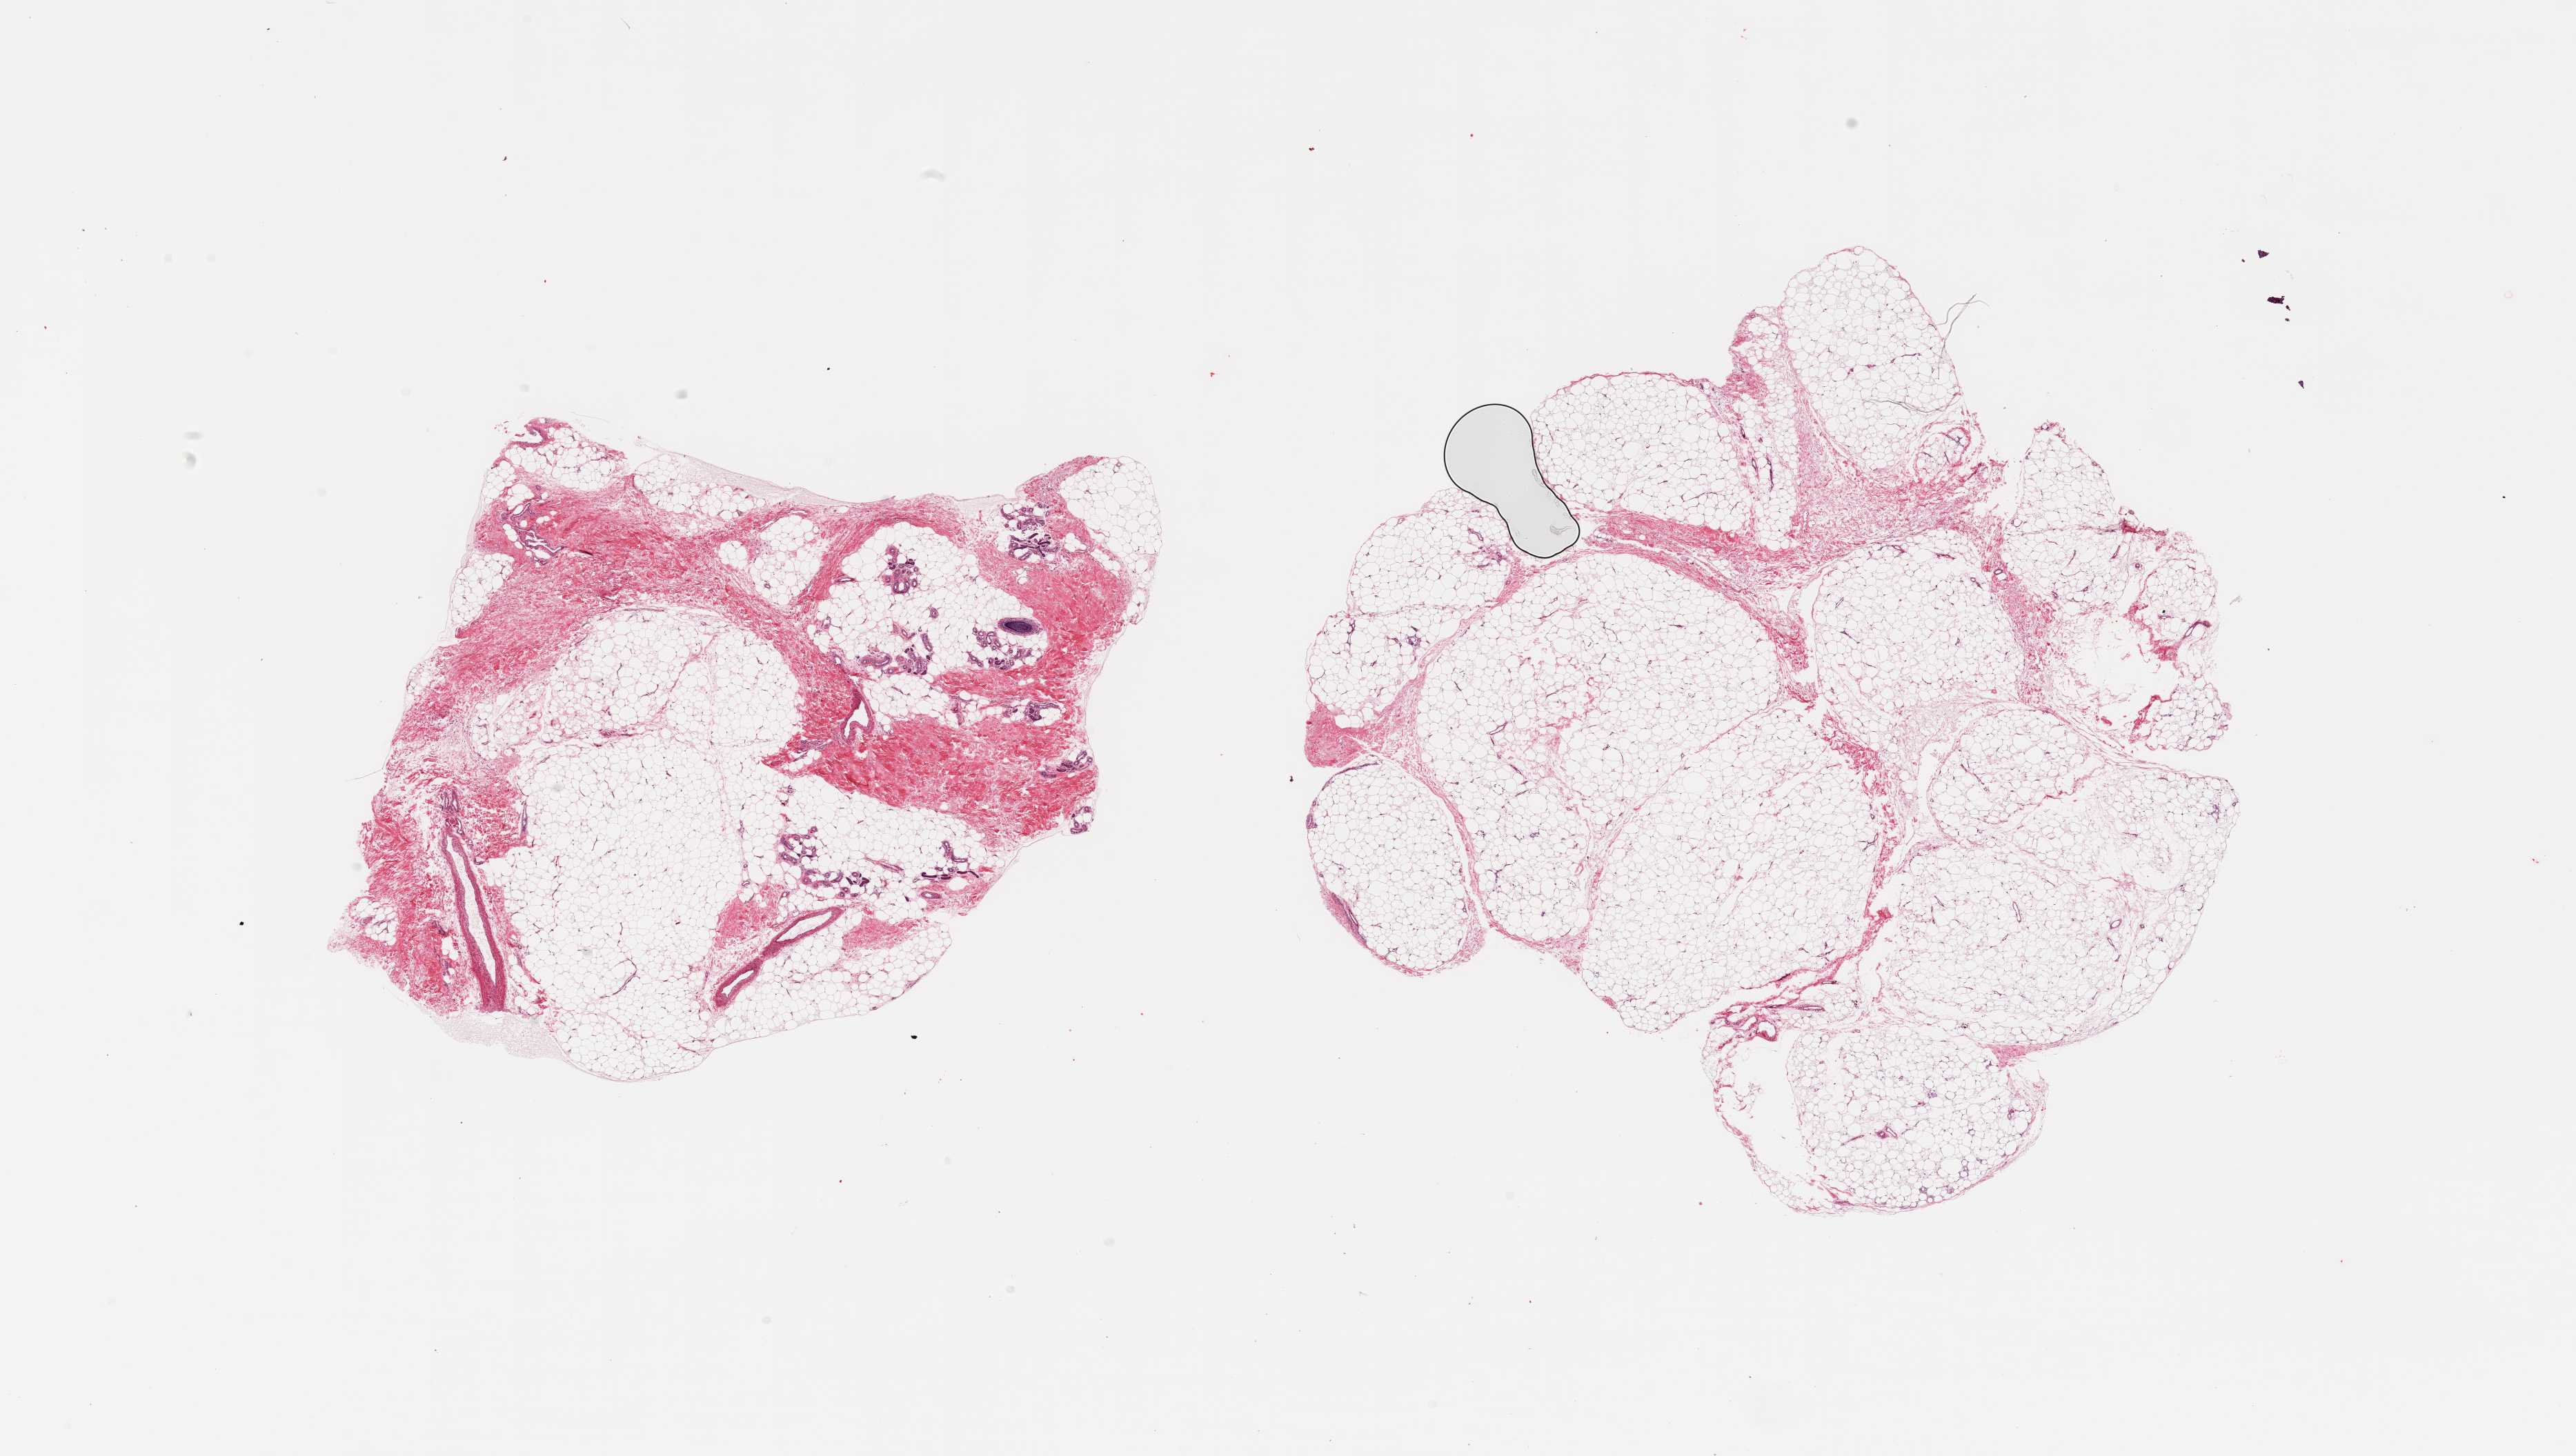
Whole-slide image, haematoxylin and eosin stain, a low-resolution overview of the entire scanned area, about 29.5 x 16.7 mm; PAXgene-fixed paraffin-embedded (PFPE) section; section of adipose tissue (target tissue); tissue donor sample. Donor sex: male.
Pathologist's review note for this sample: 2 pieces; 1 piece contains hair and sweat glands.